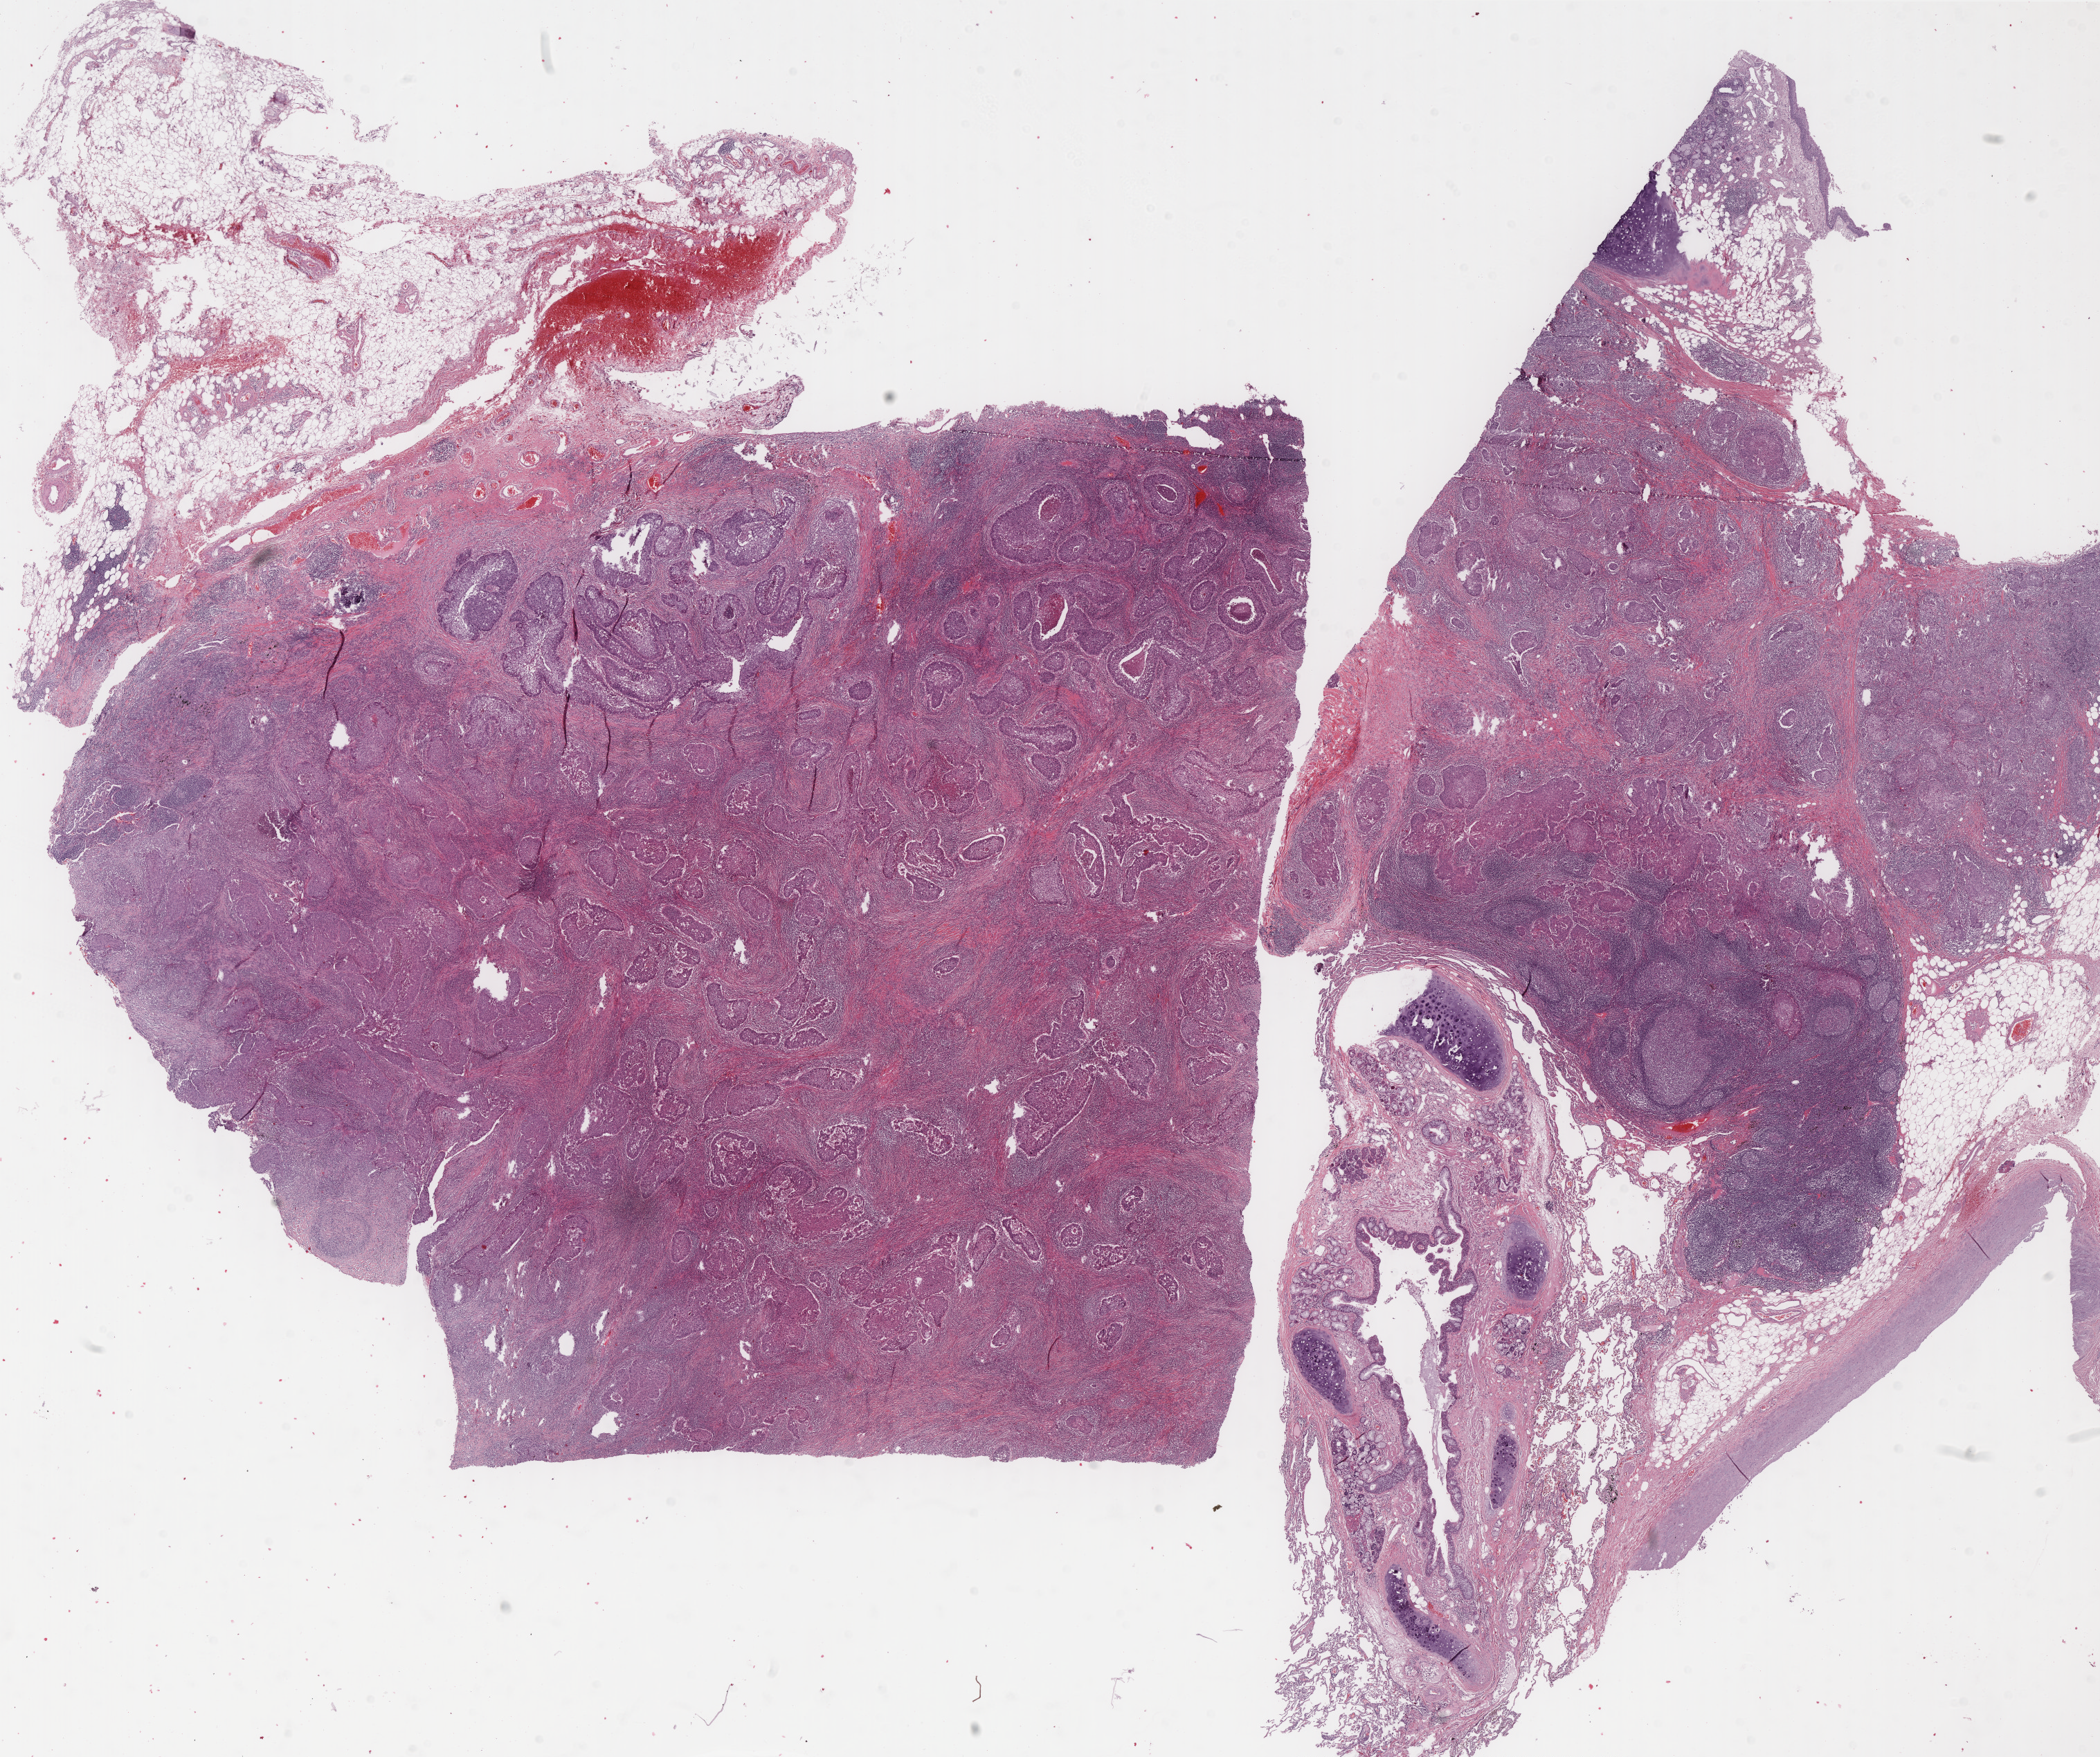
H&E-stained whole-slide image — low-resolution overview of the scanned area, about 24.4 x 20.5 mm (from a 40x scan). FFPE section. Lung, primary tumour sample. Male patient; age at initial diagnosis 61 years.
Histologic diagnosis: Squamous cell carcinoma, NOS. AJCC pathologic stage: IIB (7th edition). TNM: T2b N1 M0. Laterality: left.